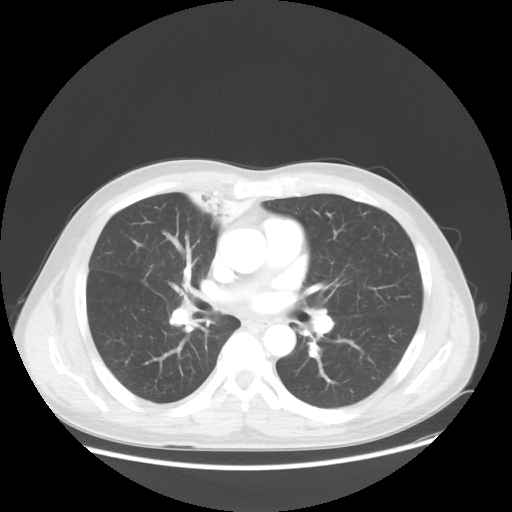
Chest CT, one axial slice; reconstruction kernel STANDARD; lung window (W 1500 / L -600 HU); 5 mm slice thickness; 512 × 512 image matrix, field of view 398 × 398 mm. Patient: male, 60 years. Case-level facts recorded for this patient, not image findings: clinical TNM (as recorded): T2a N1 M0.
Outlined on this slice (rectangle marked by the reading radiologist):
- lung tumour (recorded histology: squamous cell carcinoma): box from (x=186, y=177) to (x=257, y=239) px